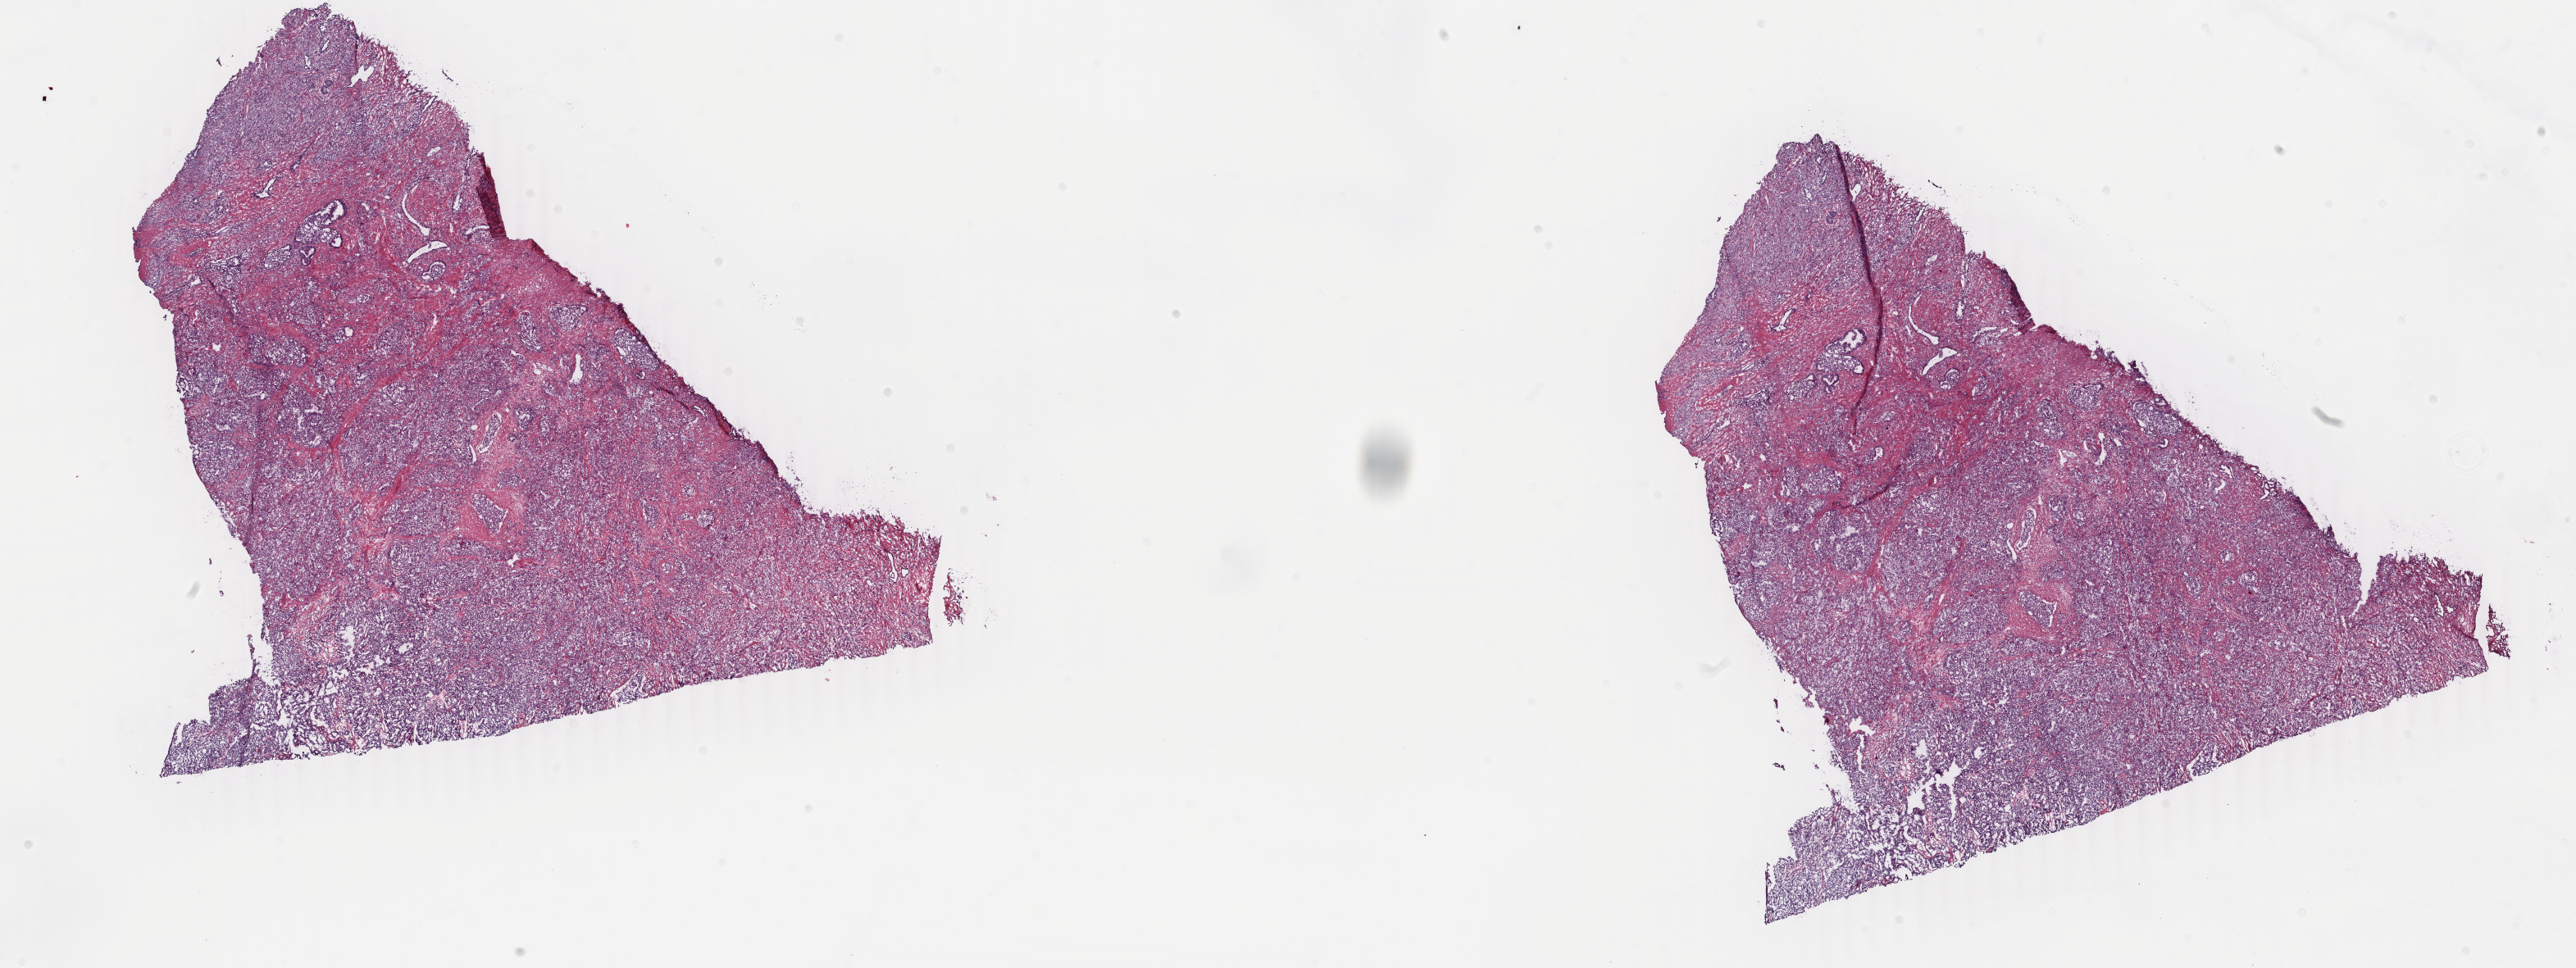
Whole-slide histology image, H&E-stained, whole scanned area (about 25.0 x 9.4 mm) shown as a low-resolution overview; frozen section from the top of the tissue portion; primary tumour sample from the prostate. Male, age 55 years at initial diagnosis. Gleason score: 9 (5+4). Composition of this section per pathologist review: tumour cells 80%, tumour nuclei 85%, normal cells 2%, stromal cells 18%, necrosis 0%. Inflammatory infiltration, as recorded: lymphocyte infiltration 0%, monocyte infiltration 0%, neutrophil infiltration 0%.
Lymph nodes positive (case pathology): 2 of 14 examined. Diagnosis: Adenocarcinoma, NOS (prostate gland).